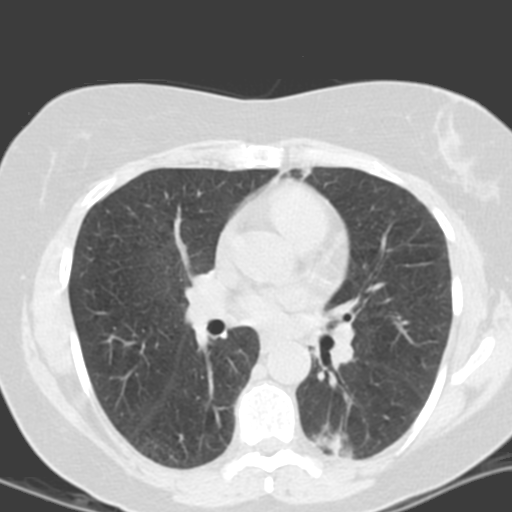
Axial slice from a low-dose chest CT screening exam, second annual screen, lung window (W 1500 / L -600 HU), 120 kVp. Female, age 55 years at enrolment.
Expert reader's lesion annotation, bounding box (x1, y1, x2, y2) in pixels: (304, 410, 379, 470). The screening reader recorded 4 non-calcified nodules or masses ≥4 mm on this exam (left lower lobe, left lower lobe, left upper lobe, right middle lobe); which of them this box marks is not recorded. Later outcome: lung cancer diagnosed 688 days after this screen — adenocarcinoma with mixed subtypes, left lower lobe, poorly differentiated (G3), stage IA (AJCC 6th edition), 21 mm at pathology.